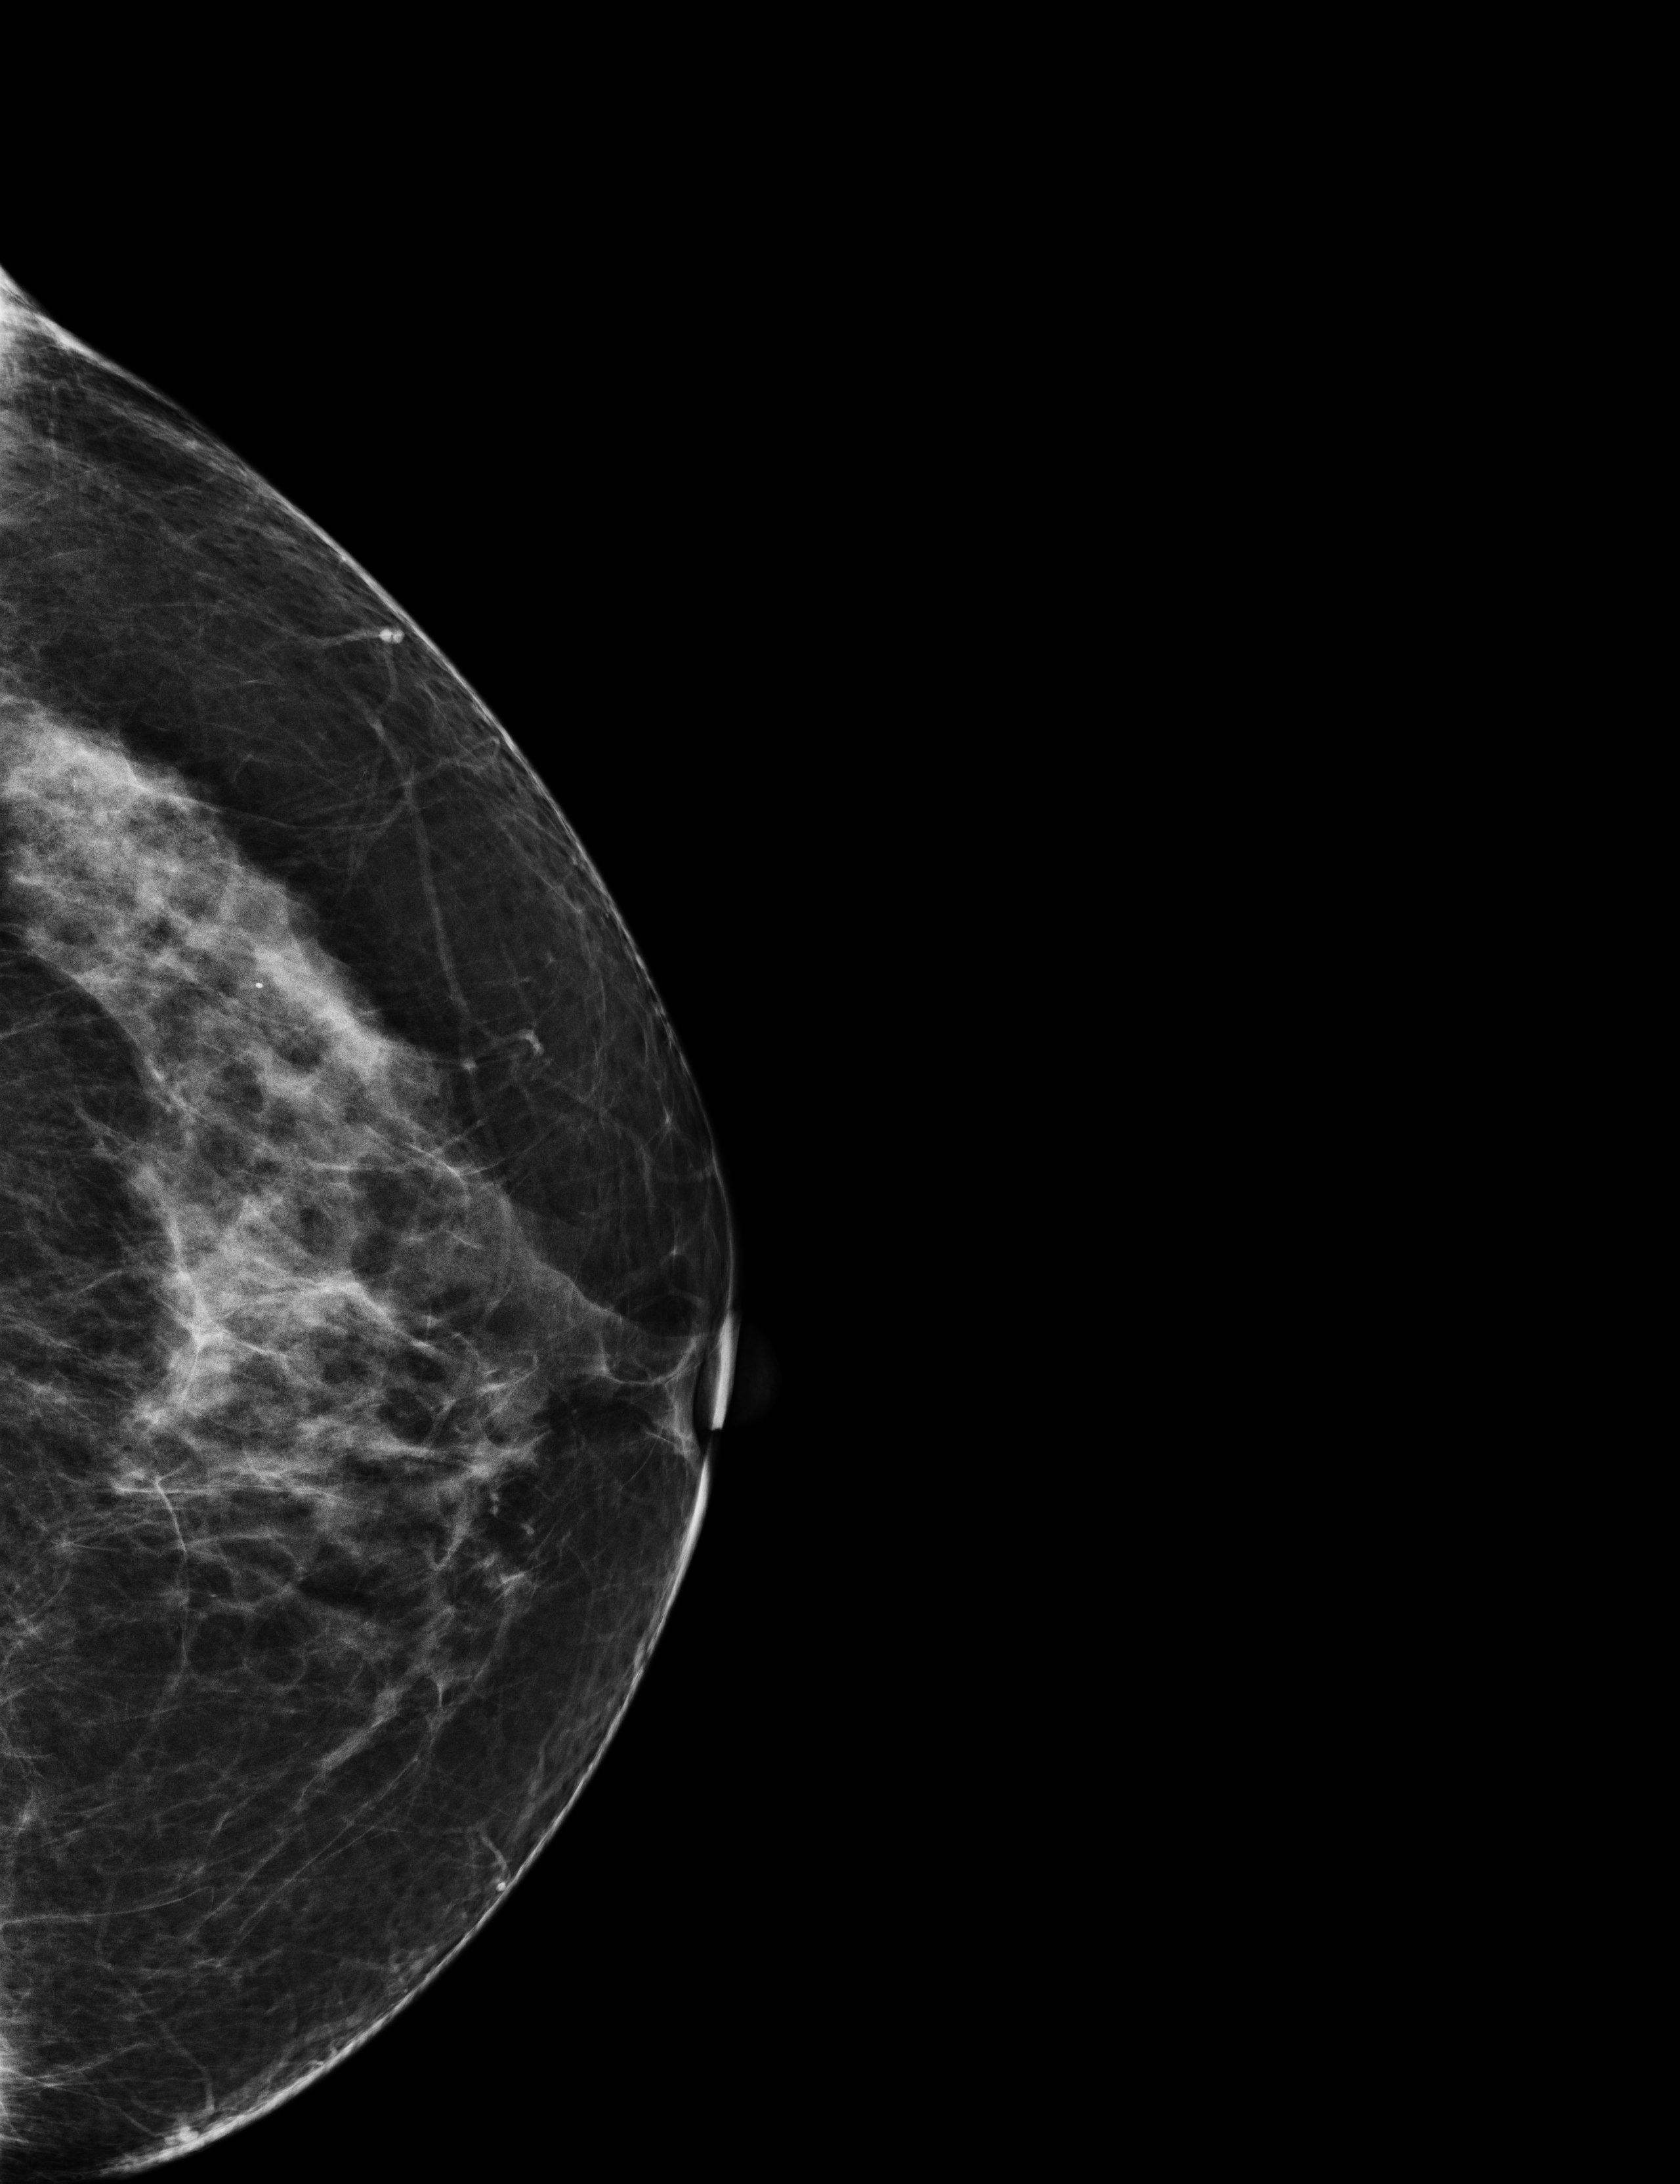
Digital mammogram (FFDM); left breast; craniocaudal (CC) view; annual screening mammography examination. Female patient, age 63 years.
Breast density at the screening exam (both breasts): heterogeneously dense (BI-RADS density category c). Final BI-RADS assessment for this screening round (tomosynthesis exam, both breasts): category 1. Recall: no recall after this screen.